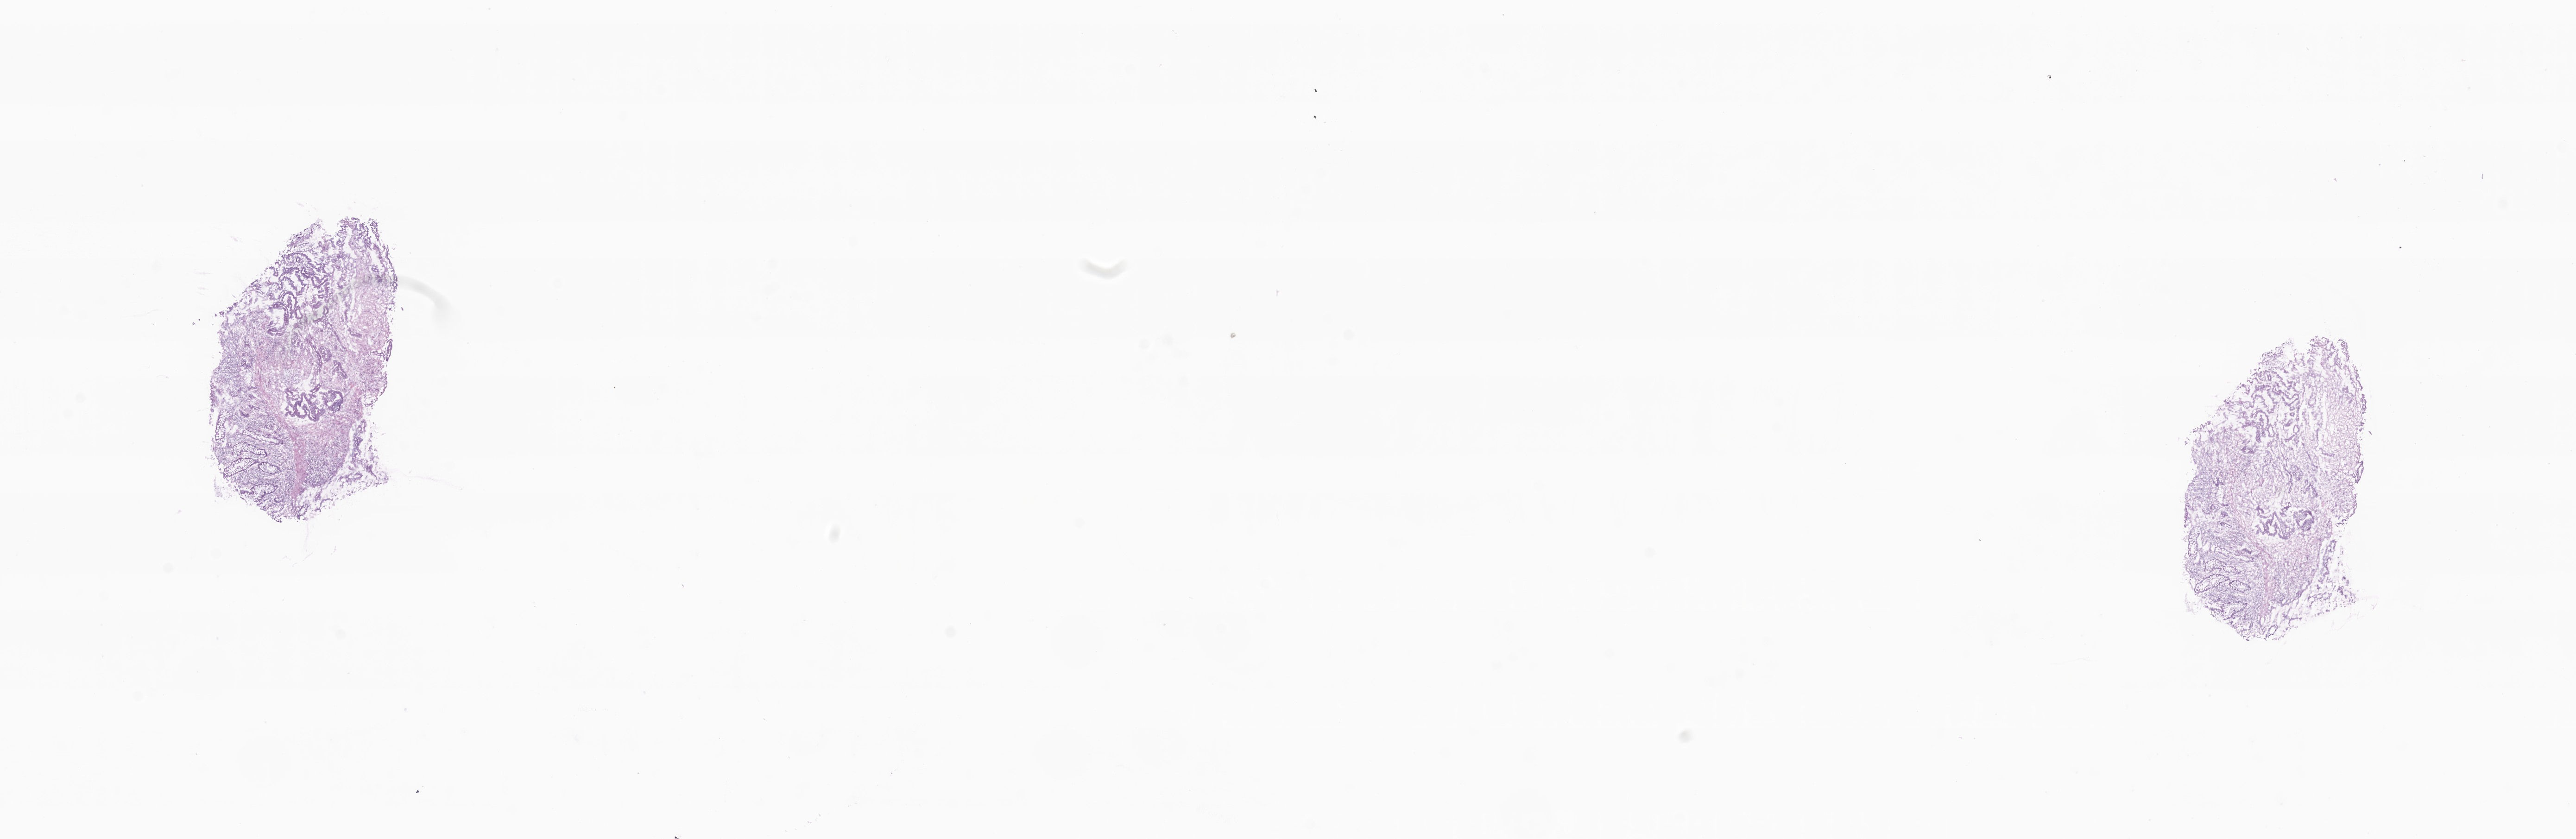
Digitized H&E-stained section, shown as a low-resolution overview of the whole scanned area (about 23.4 x 7.6 mm). Cryosection. Primary tumor. Anatomic site: hepatic flexure of colon. Male, age 70 years at initial diagnosis. Composition of this section per pathologist review: tumor cells 40%, tumor nuclei 60%, stromal cells 30%, necrosis 0%, normal cells 30%. Inflammatory infiltration, as recorded: lymphocyte infiltration 100%, monocyte infiltration 0%, neutrophil infiltration 0%.
• histologic diagnosis: Adenocarcinoma, NOS